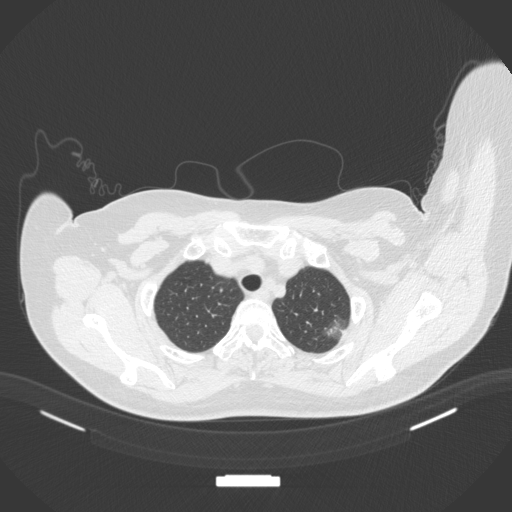
Chest CT, one axial slice; position 319 of 386 along the scan axis; reconstruction kernel B31f; lung window (W 1500 / L -600 HU); 1 mm slice thickness; 512 × 512 image matrix. Female patient, age 58 years. From the clinical record (not read from this slice): clinical TNM (as recorded): T1c N0 M0.
Structures marked on this image (rectangle marked by the reading radiologist):
- lung tumour (recorded histology: adenocarcinoma): bounding box <320,315,352,341> (left, top, right, bottom; pixels)